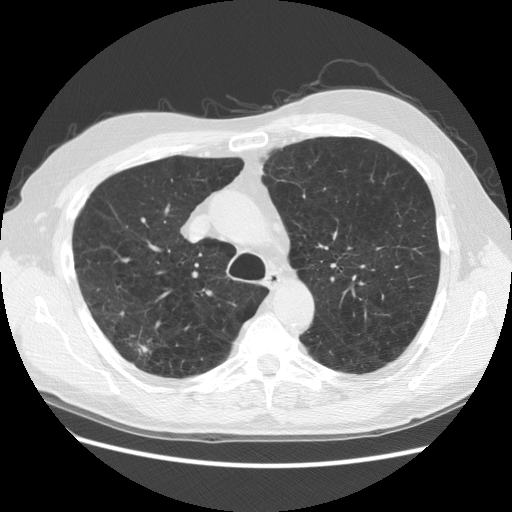
Low-dose screening chest CT, one axial slice. Position 96 of 137 along the scan axis. Lung window (W 1500 / L -600 HU). 2.5 mm slice thickness. 512 × 512 image matrix, field of view 377 × 377 mm.
Annotated regions visible in this slice (outlined manually by an expert reader):
- lesion 2 (nodule, upper lobe of right lung): bounding box <137,342,150,355> (left, top, right, bottom; pixels)